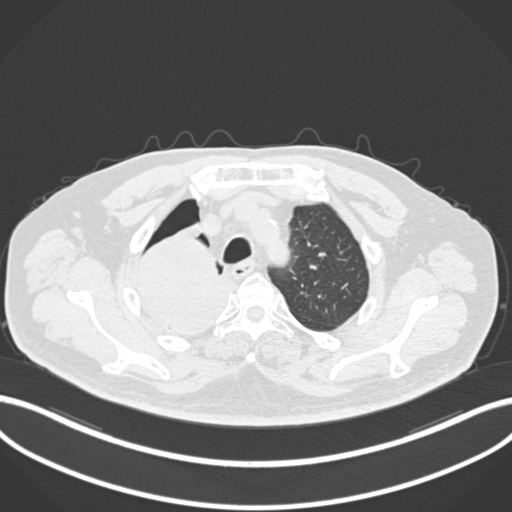
Chest CT, one axial slice. Slice 172 of 218 in the series (ordered by position). Reconstruction kernel B30f. Lung window (W 1500 / L -600 HU). 1 mm slice thickness. 512 × 512 image matrix, field of view 400 × 400 mm. Patient: male, 68 years. From the clinical record (not read from this slice): clinical TNM (as recorded): T2a N0 M0.
Structures marked on this image (bounding box drawn by a radiologist):
- lung tumour (recorded histology: adenocarcinoma): bounding box <128,226,236,334> (left, top, right, bottom; pixels)